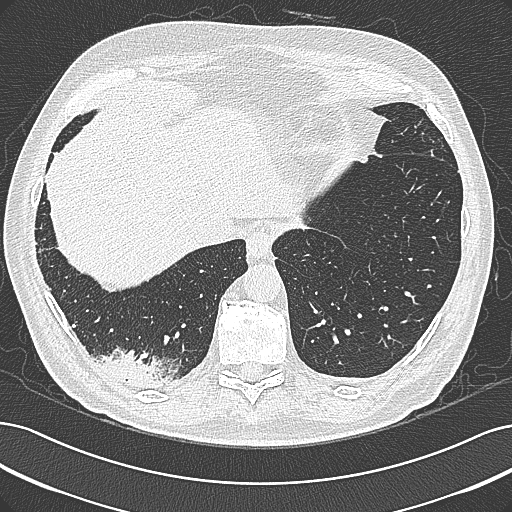
Chest CT (low-dose screening protocol), one axial image, baseline annual screen, lung window (W 1500 / L -600 HU), 1 mm slice thickness, lung (sharp) reconstruction kernel (B80f). Male participant, aged 68 years at enrolment. Former smoker at enrolment.
Expert reader's lesion annotation, box from (x=96, y=340) to (x=186, y=401) px. No non-calcified nodule or mass ≥4 mm was recorded by the screening reader at this exam. Official screen result: negative screen, significant abnormalities not suspicious for lung cancer. Participant outcome: lung cancer diagnosed 154 days after this screen — mucinous adenocarcinoma, right lower lobe, well differentiated (G1), stage IB (AJCC 6th edition), 50 mm at pathology.